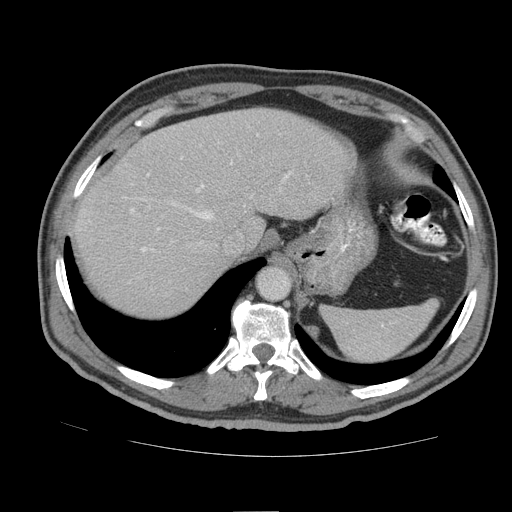
Contrast-enhanced abdominal CT (liver protocol), one axial slice; position 68 of 105 along the scan axis; soft-tissue window (W 400 / L 40 HU); 2.5 mm slice thickness; 512 × 512 image matrix, field of view 380 × 380 mm. From the clinical record (not read from this slice): diagnosis: hepatocellular carcinoma (patient treated with transarterial chemoembolisation; whether this scan precedes or follows treatment is not stated here); TNM stage (as recorded): Stage-IIIB; Child-Pugh class: A.
Outlined on this slice (semi-automatic segmentation, software-assisted and operator-edited):
- abdominal aorta: bounding box (x1, y1, x2, y2) in pixels: (258, 268, 289, 298)
- liver parenchyma outside the tumour (the mass and vessels are separate outlines, so this box may not span the whole liver): (72, 108, 356, 316)
- liver vessels: (131, 173, 289, 252)